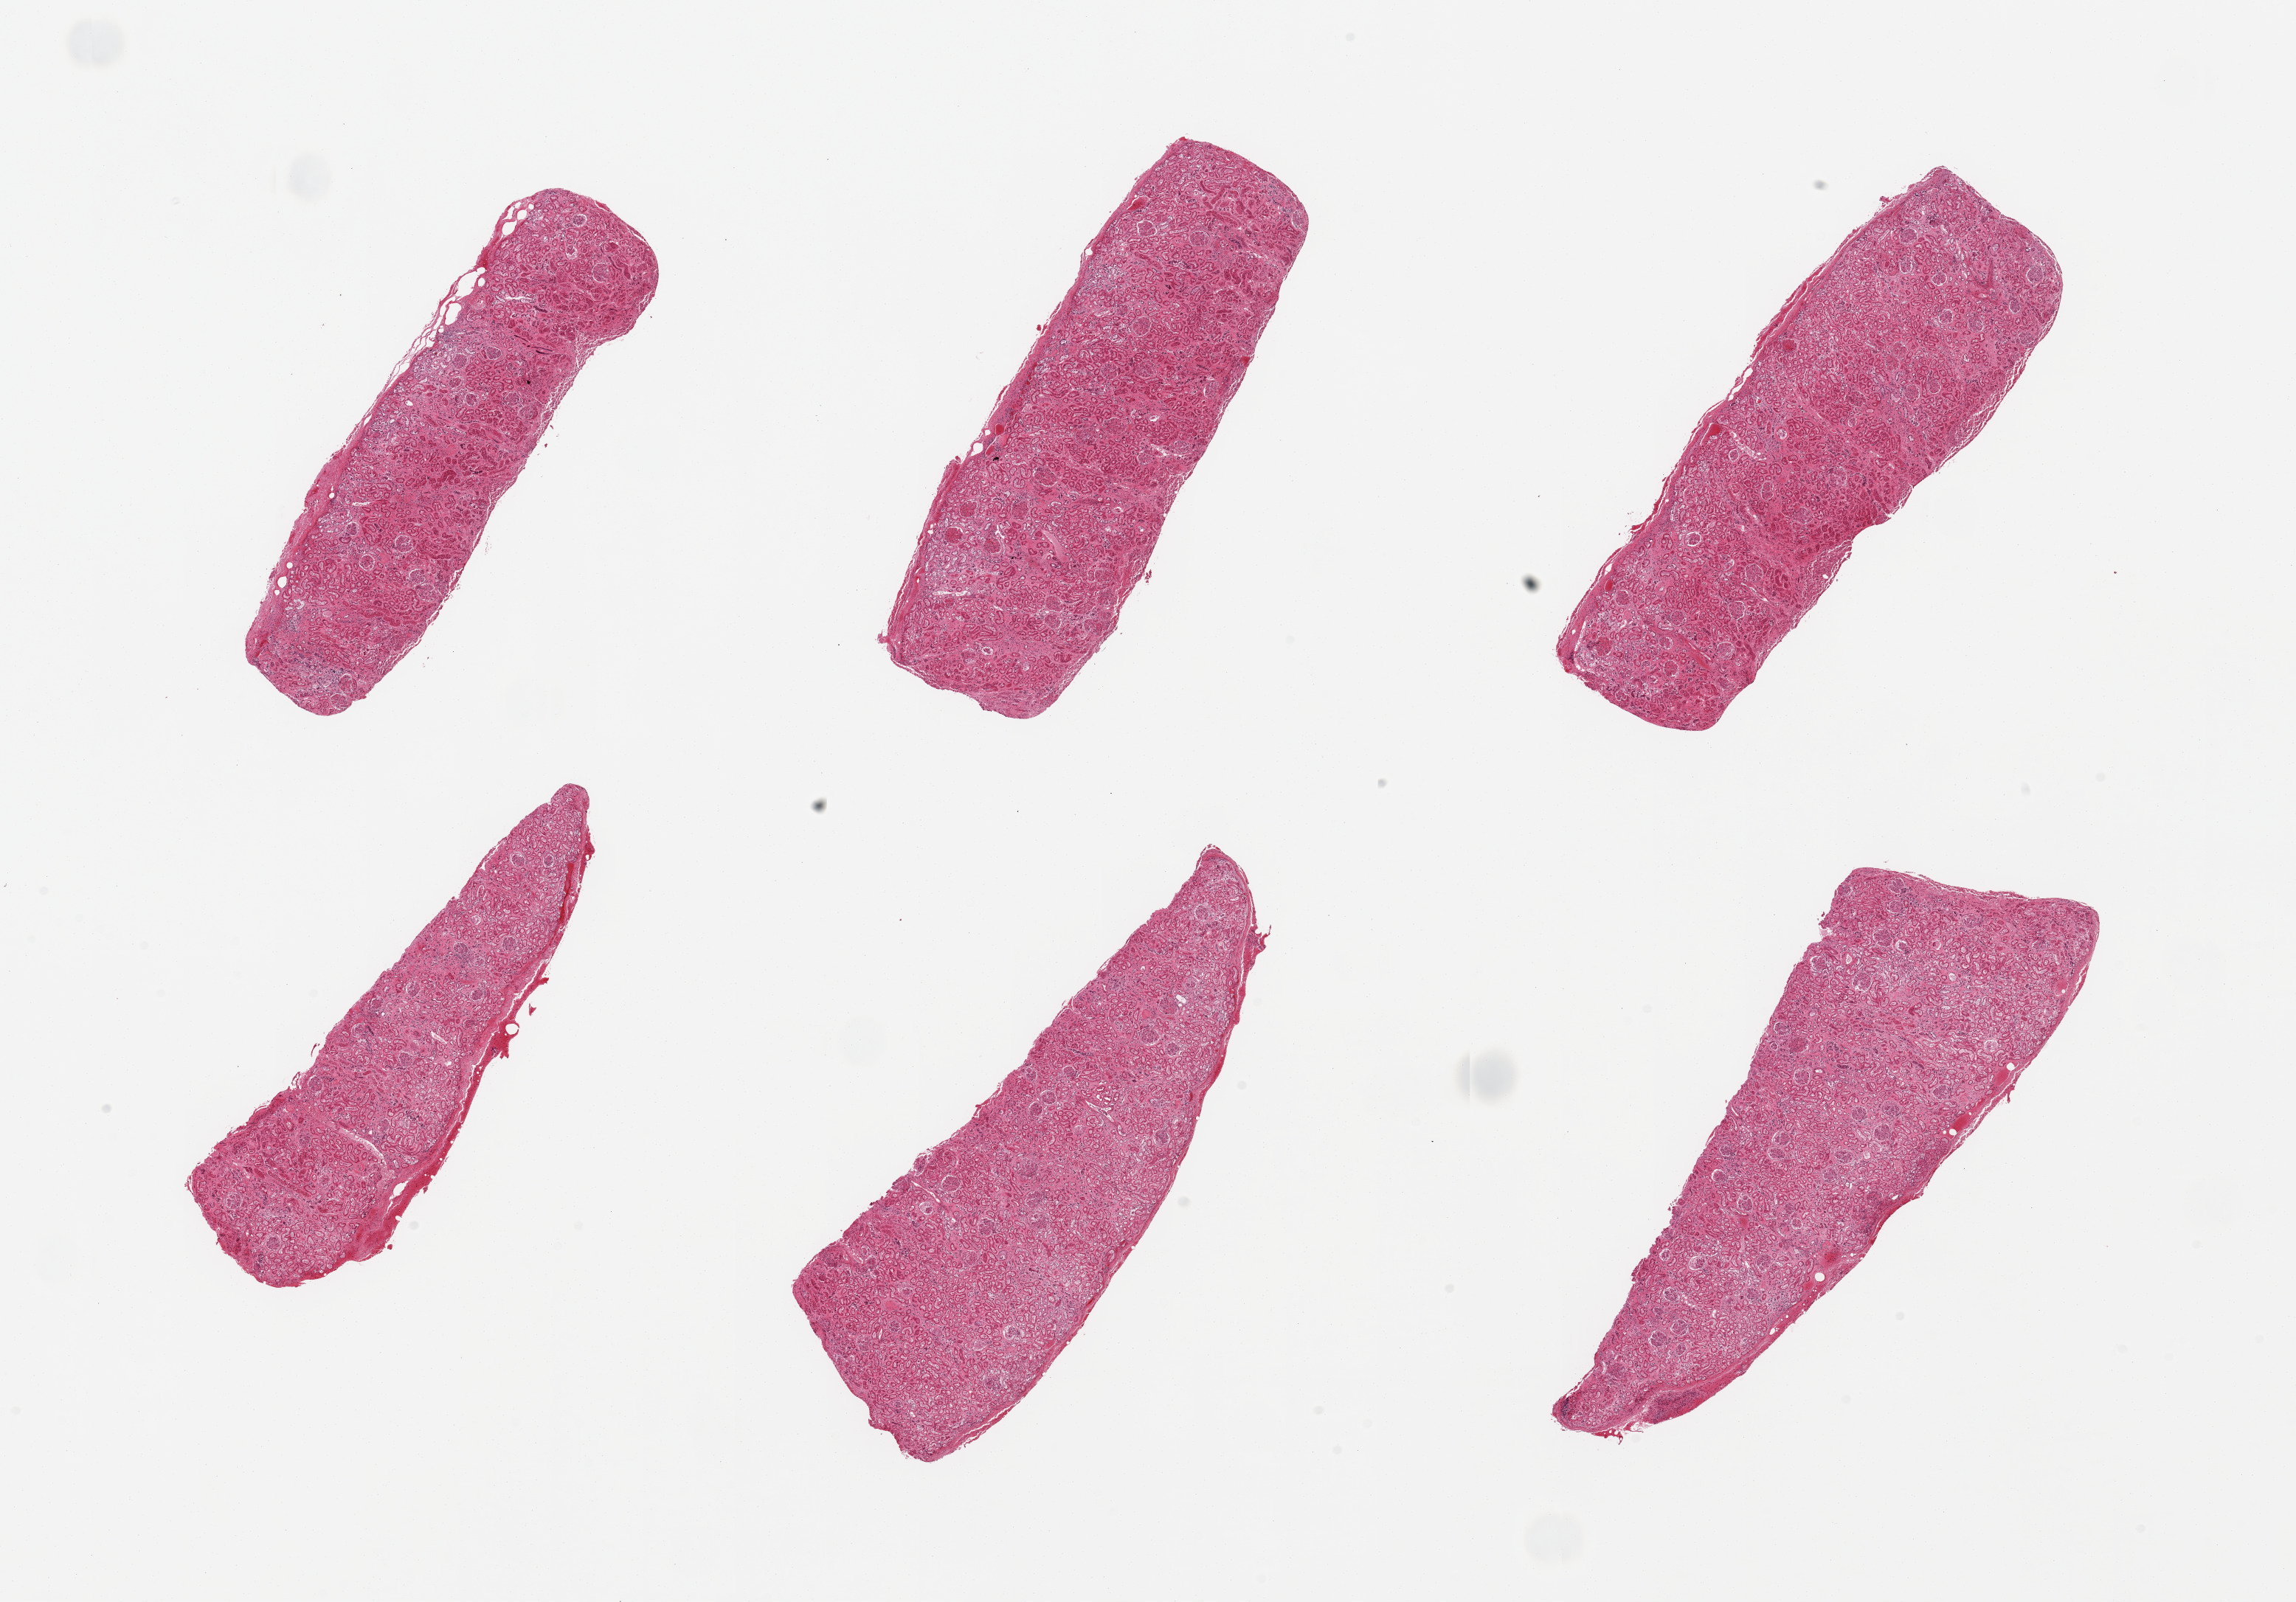
Hematoxylin and eosin (H&E) whole-slide image — low-resolution overview of the scanned area, about 24.6 x 17.2 mm; PAXgene-fixed, paraffin-embedded tissue; sampled site (target tissue): renal cortex; tissue donor sample. Donor: male.
* pathologist's review note for this sample: 6 pieces; renal cortex with scattered hyalinized glomeruli; sloughing distal tubular epithelium